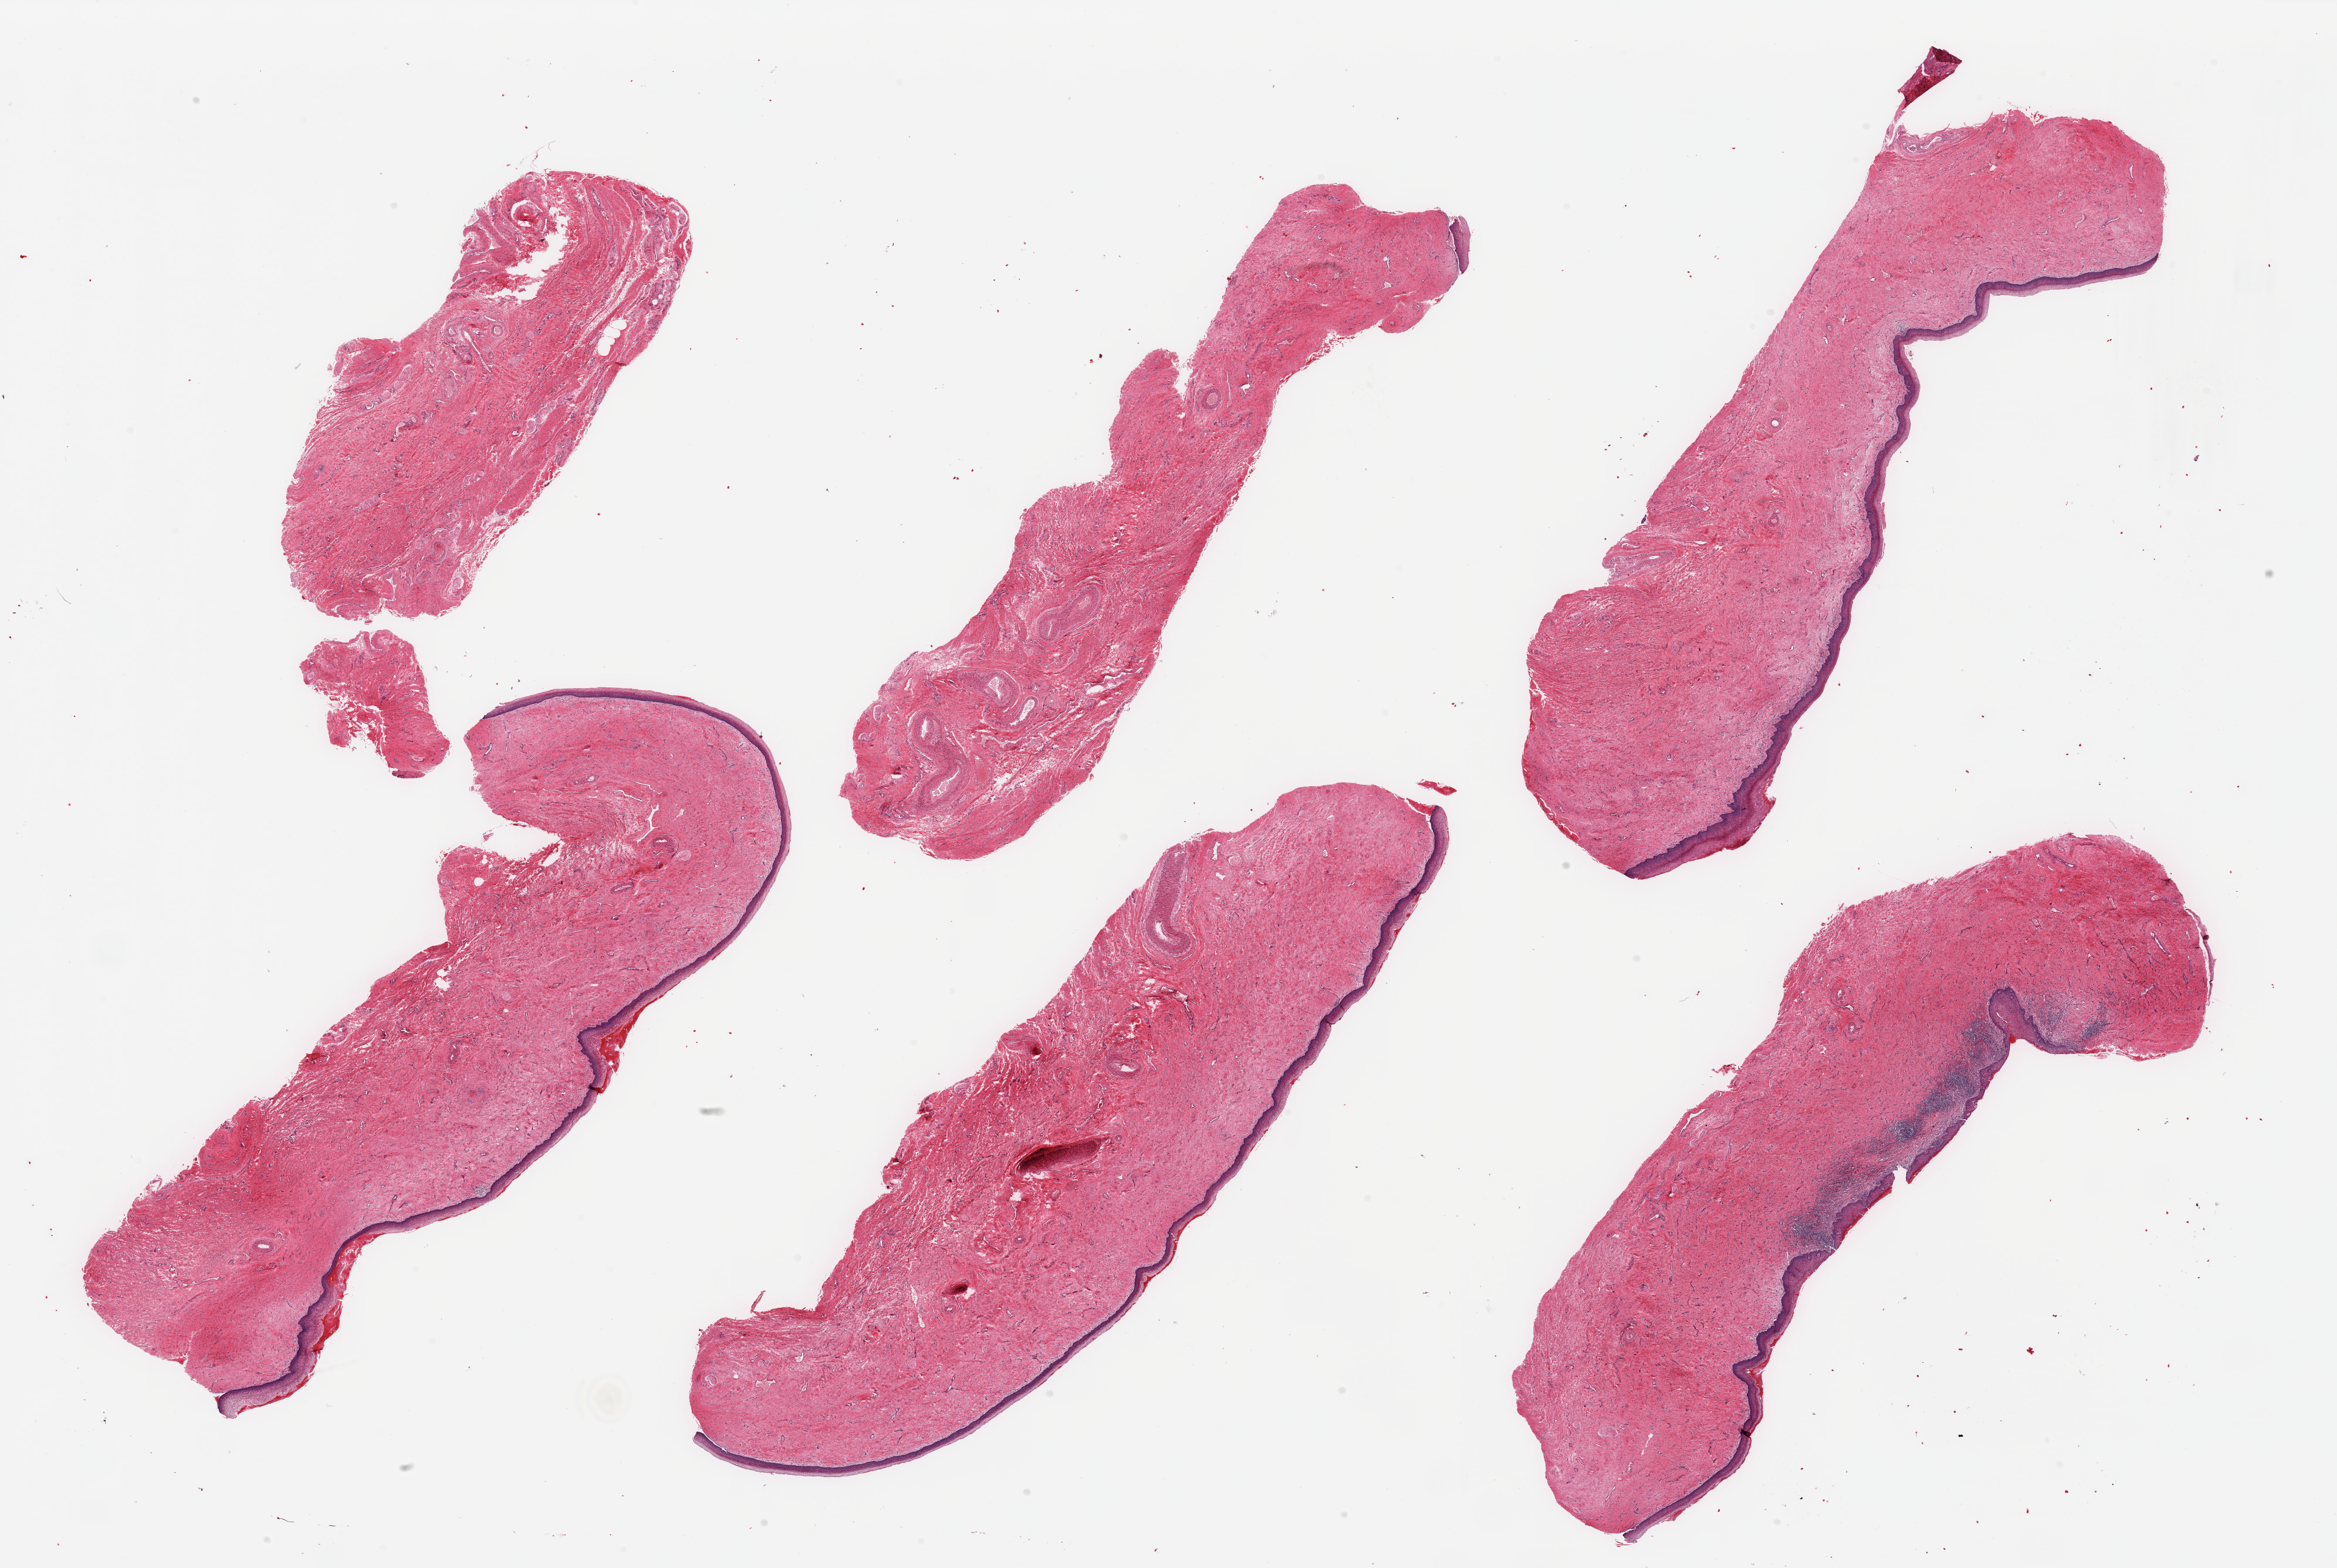
Digitized haematoxylin and eosin-stained section, shown as a low-resolution overview of the whole scanned area (about 31.5 x 21.1 mm). PAXgene-fixed paraffin-embedded (PFPE) section. Target tissue: vagina. Donor tissue sample. Donor: female.
Pathologist's review note for this sample: 6 pieces; 5 pieces include squamous mucosa, 1 shows chronic inflammation.